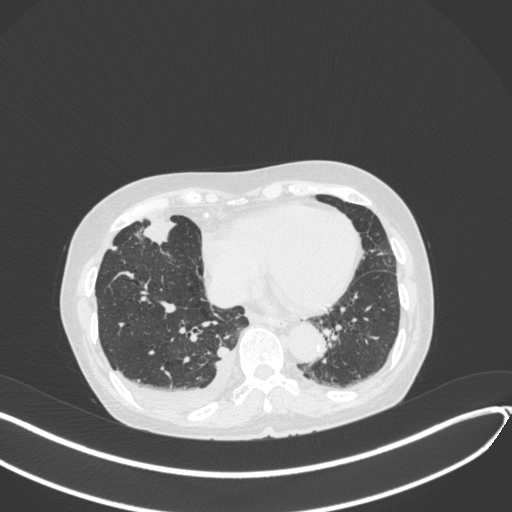
Chest CT, one axial slice; position 121 of 418 along the scan axis; lung window (W 1500 / L -600 HU); 512 × 512 image matrix, field of view 400 × 400 mm. Patient: female, 75 years. Case-level facts recorded for this patient, not image findings: clinical TNM (as recorded): T2a N3 M0.
Annotated regions visible in this slice (bounding box drawn by a radiologist):
- lung tumour (recorded histology: adenocarcinoma): bounding box (x1, y1, x2, y2) in pixels: (140, 218, 183, 249)